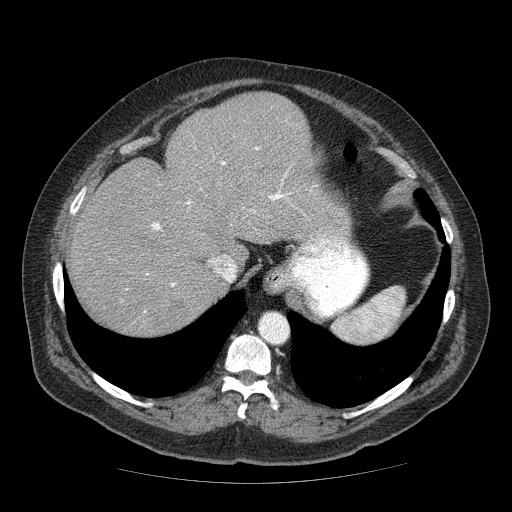
Contrast-enhanced abdominal CT (liver protocol), one axial slice. Position 51 of 85 along the scan axis. 120 kVp. Soft-tissue window (W 400 / L 40 HU). 2.5 mm slice thickness. 512 × 512 image matrix. From the clinical record (not read from this slice): diagnosis: hepatocellular carcinoma (patient treated with transarterial chemoembolisation; whether this scan precedes or follows treatment is not stated here); TNM stage (as recorded): Stage-IIIA.
Annotated regions visible in this slice (semi-automatic segmentation, software-assisted and operator-edited):
- abdominal aorta: bounding box (x1, y1, x2, y2) in pixels: (259, 313, 288, 343)
- liver parenchyma outside the tumour (the mass and vessels are separate outlines, so this box may not span the whole liver): (68, 92, 350, 336)
- liver vessels: (152, 147, 305, 287)